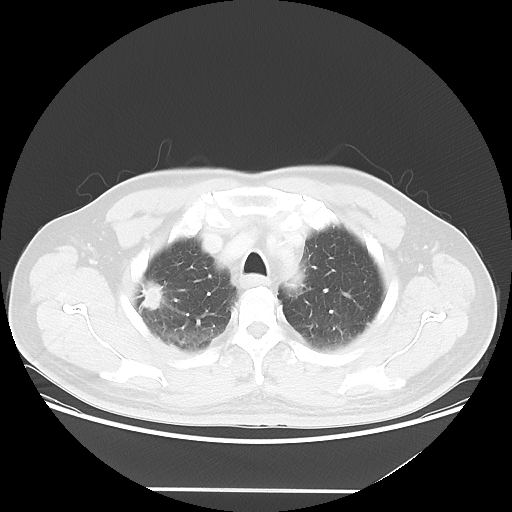
Chest CT, one axial slice. Position 44 of 54 along the scan axis. Reconstruction kernel LUNG. Lung window (W 1500 / L -600 HU). 5 mm slice thickness. 512 × 512 image matrix, field of view 416 × 416 mm. Male patient, age 65 years. Case-level facts recorded for this patient, not image findings: clinical TNM (as recorded): T1c N1 M0.
Outlined on this slice (rectangle marked by the reading radiologist):
- lung tumour (recorded histology: adenocarcinoma): bounding box (x1, y1, x2, y2) in pixels: (137, 275, 164, 318)